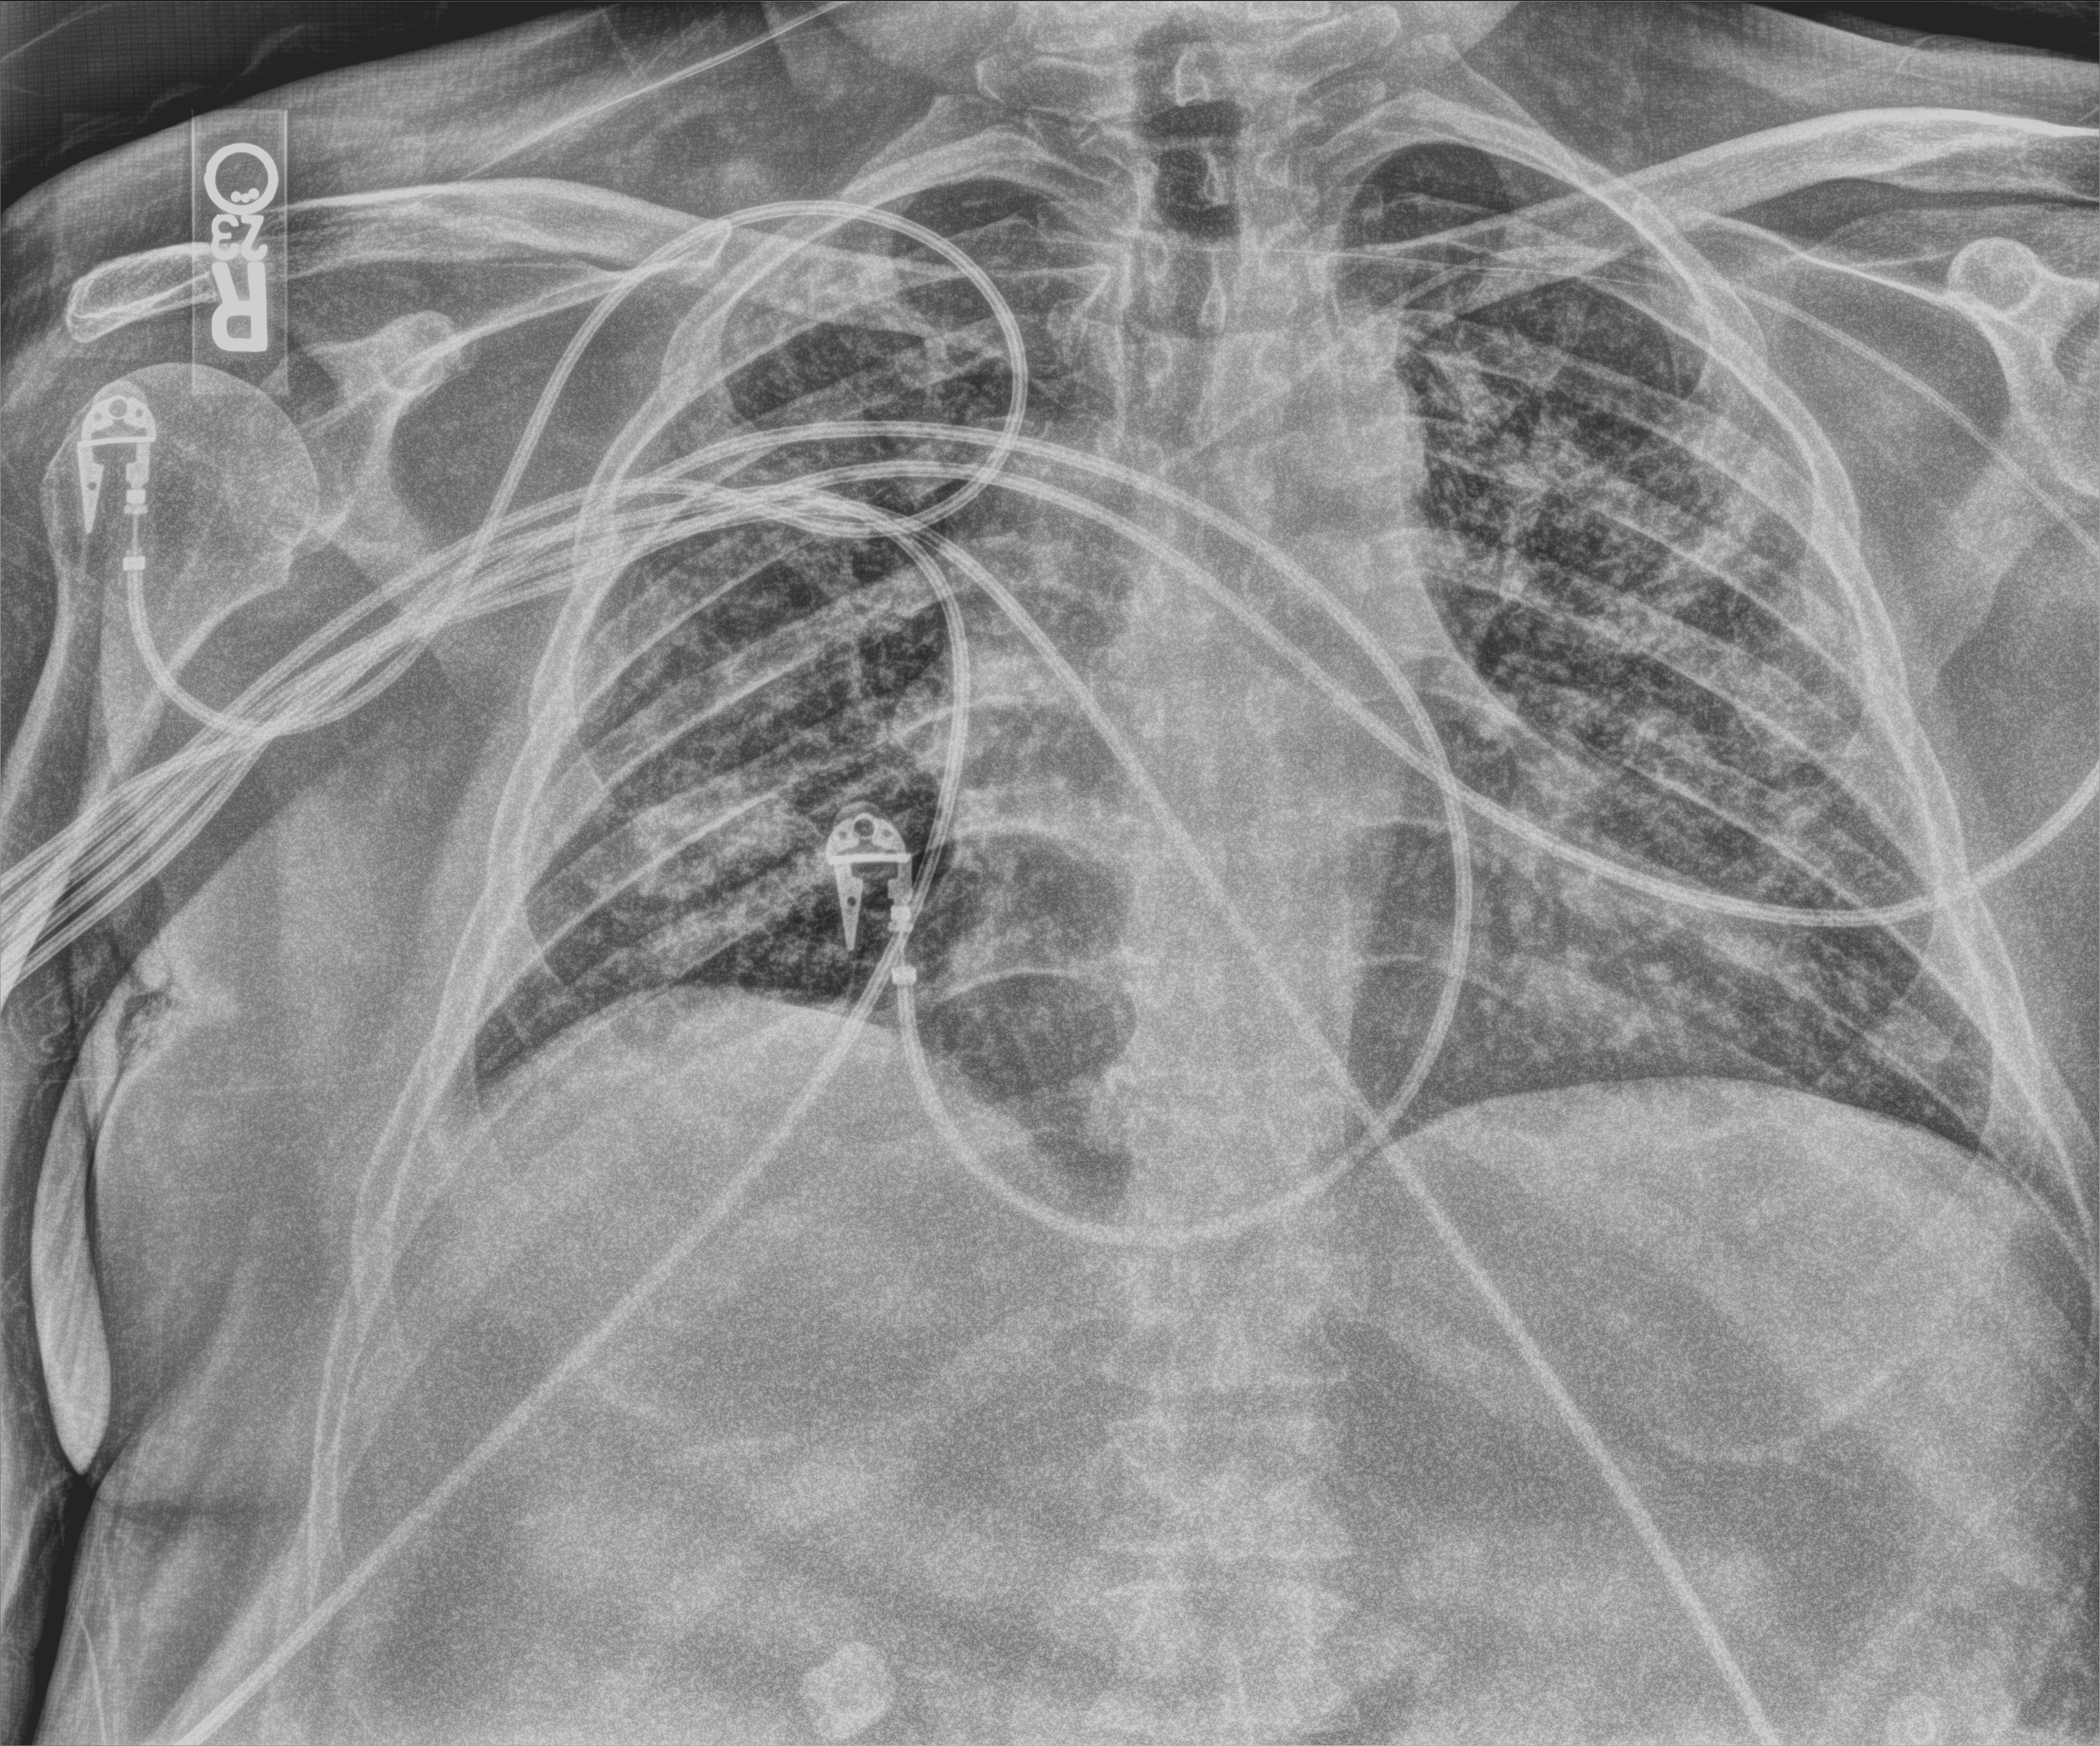
Portable chest radiograph. Patient hospitalised with COVID-19; male, aged 18–59 years.
From the hospital-stay record, not from the radiograph (when in the stay this image was taken is not recorded): other chronic lung disease (admission record): no; chronic kidney disease (admission record): no; diabetes (admission record): no.